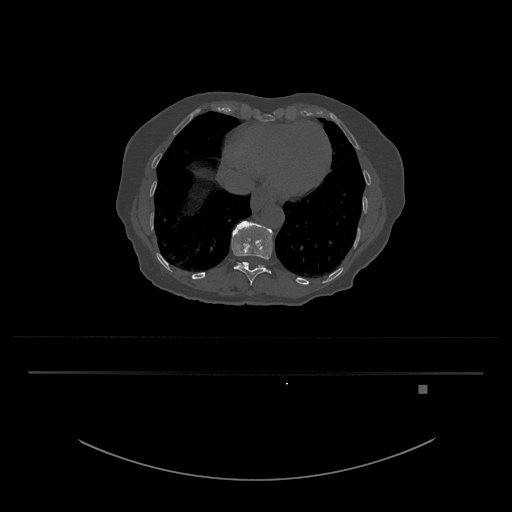
CT including the spine, one axial slice. 120 kVp. Bone window (W 1800 / L 400 HU). 0.5 mm slice thickness. 512 × 512 image matrix. Female patient, age 57 years. Case-level facts recorded for this patient, not image findings: primary cancer: cervical.
Structures marked on this image (semi-automatic segmentation, software-assisted and operator-edited):
- T11 vertebra: bounding box <231,221,273,285> (left, top, right, bottom; pixels)
- T12 vertebra: <236,262,266,270>